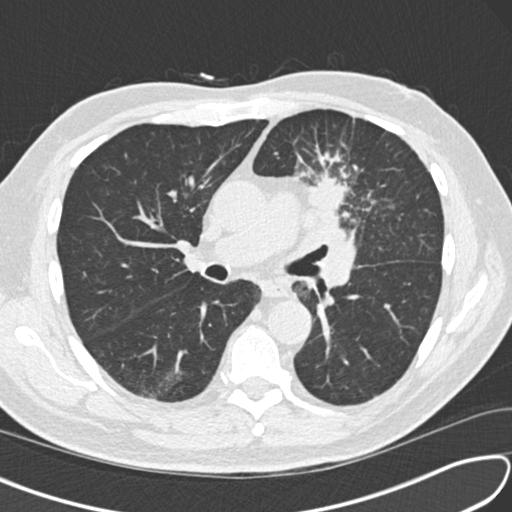
Low-dose screening chest CT, one axial slice. Position 89 of 156 along the scan axis. 120 kVp. Lung window (W 1500 / L -600 HU). 2 mm slice thickness. 512 × 512 image matrix, field of view 340 × 340 mm.
Structures marked on this image (outlined manually by an expert reader):
- lesion 1 (tumor, upper lobe of left lung): box from (x=310, y=172) to (x=346, y=227) px